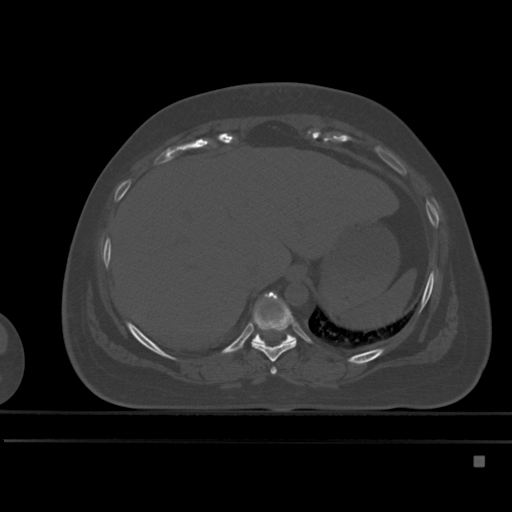
CT including the spine, one axial slice; position 258 of 495 along the scan axis; bone window (W 1800 / L 400 HU); 1.5 mm slice thickness; 512 × 512 image matrix. Female patient, age 33 years. From the clinical record (not read from this slice): primary cancer: breast; vertebrae with lytic lesions (as recorded): T1.
Annotated regions visible in this slice (semi-automatic segmentation, software-assisted and operator-edited):
- T10 vertebra: bounding box <252,330,296,344> (left, top, right, bottom; pixels)
- T8 vertebra: <271,367,277,375>
- T9 vertebra: <250,292,297,362>